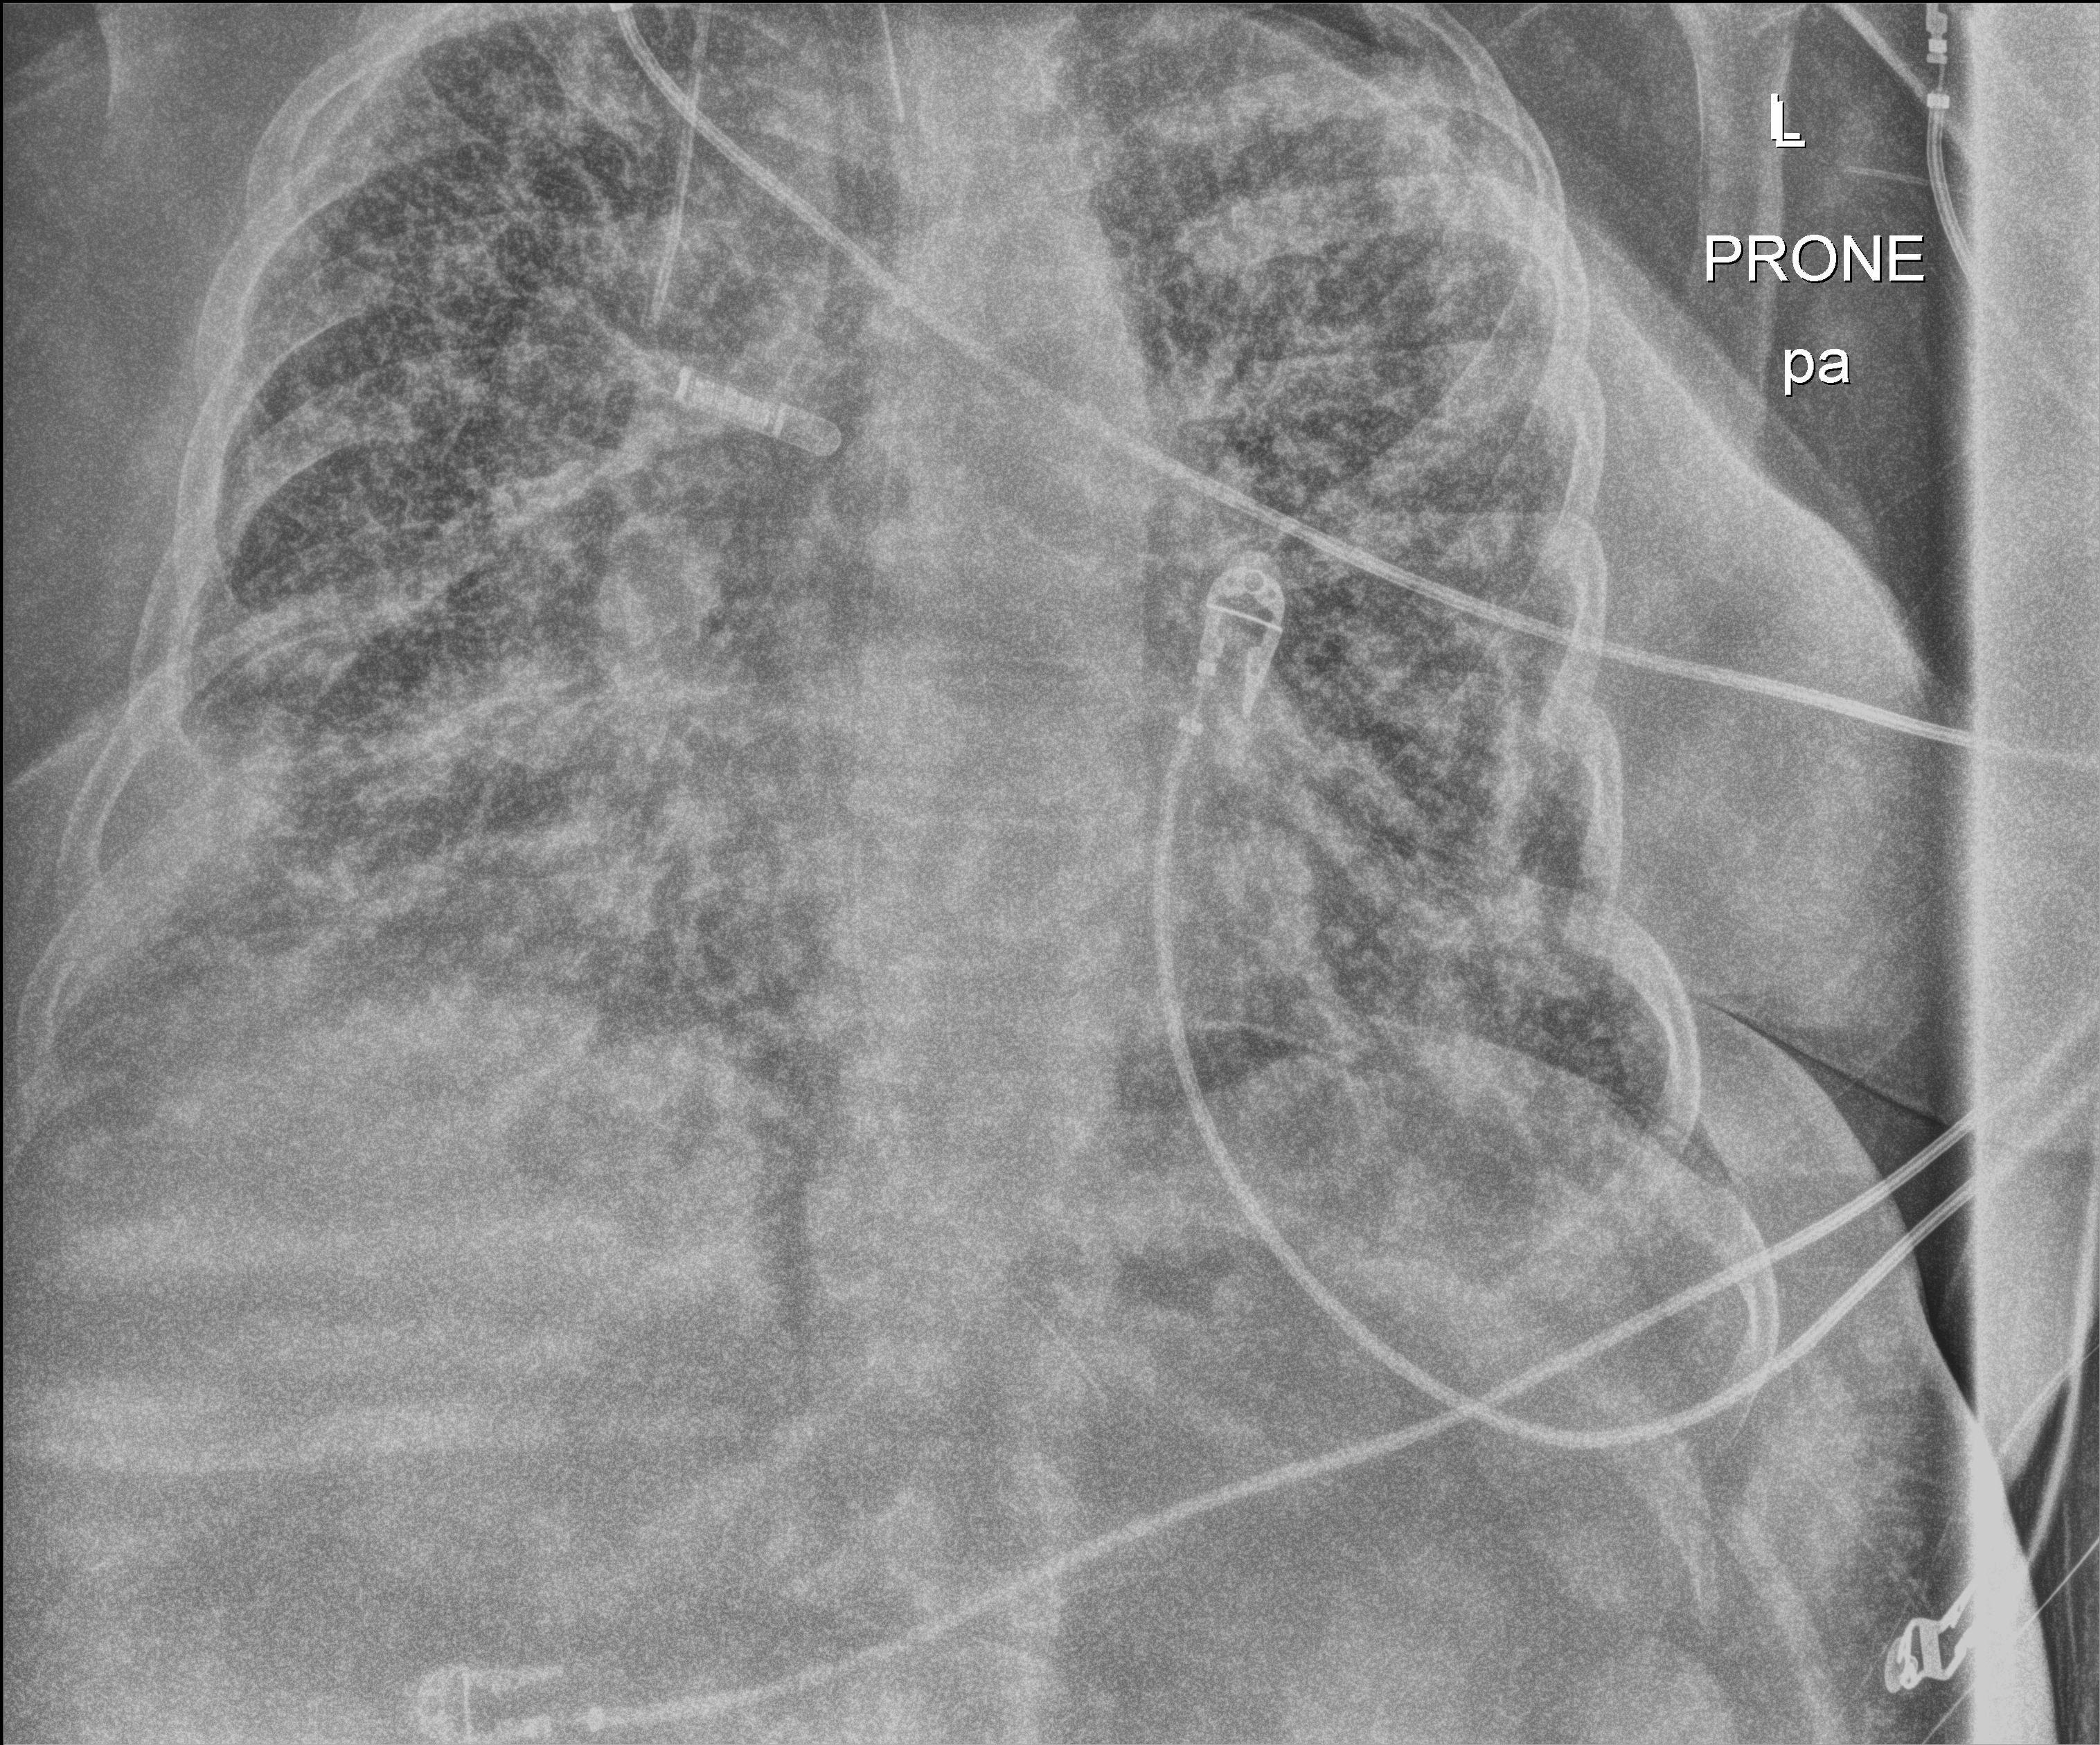
Bedside chest radiograph (digital radiography); anteroposterior (AP) projection. Patient hospitalised with COVID-19; female, aged 60–74 years.
Hospital-stay facts (about this admission, not read from this image; timing relative to this image not recorded):
- length of hospital stay: 28 days